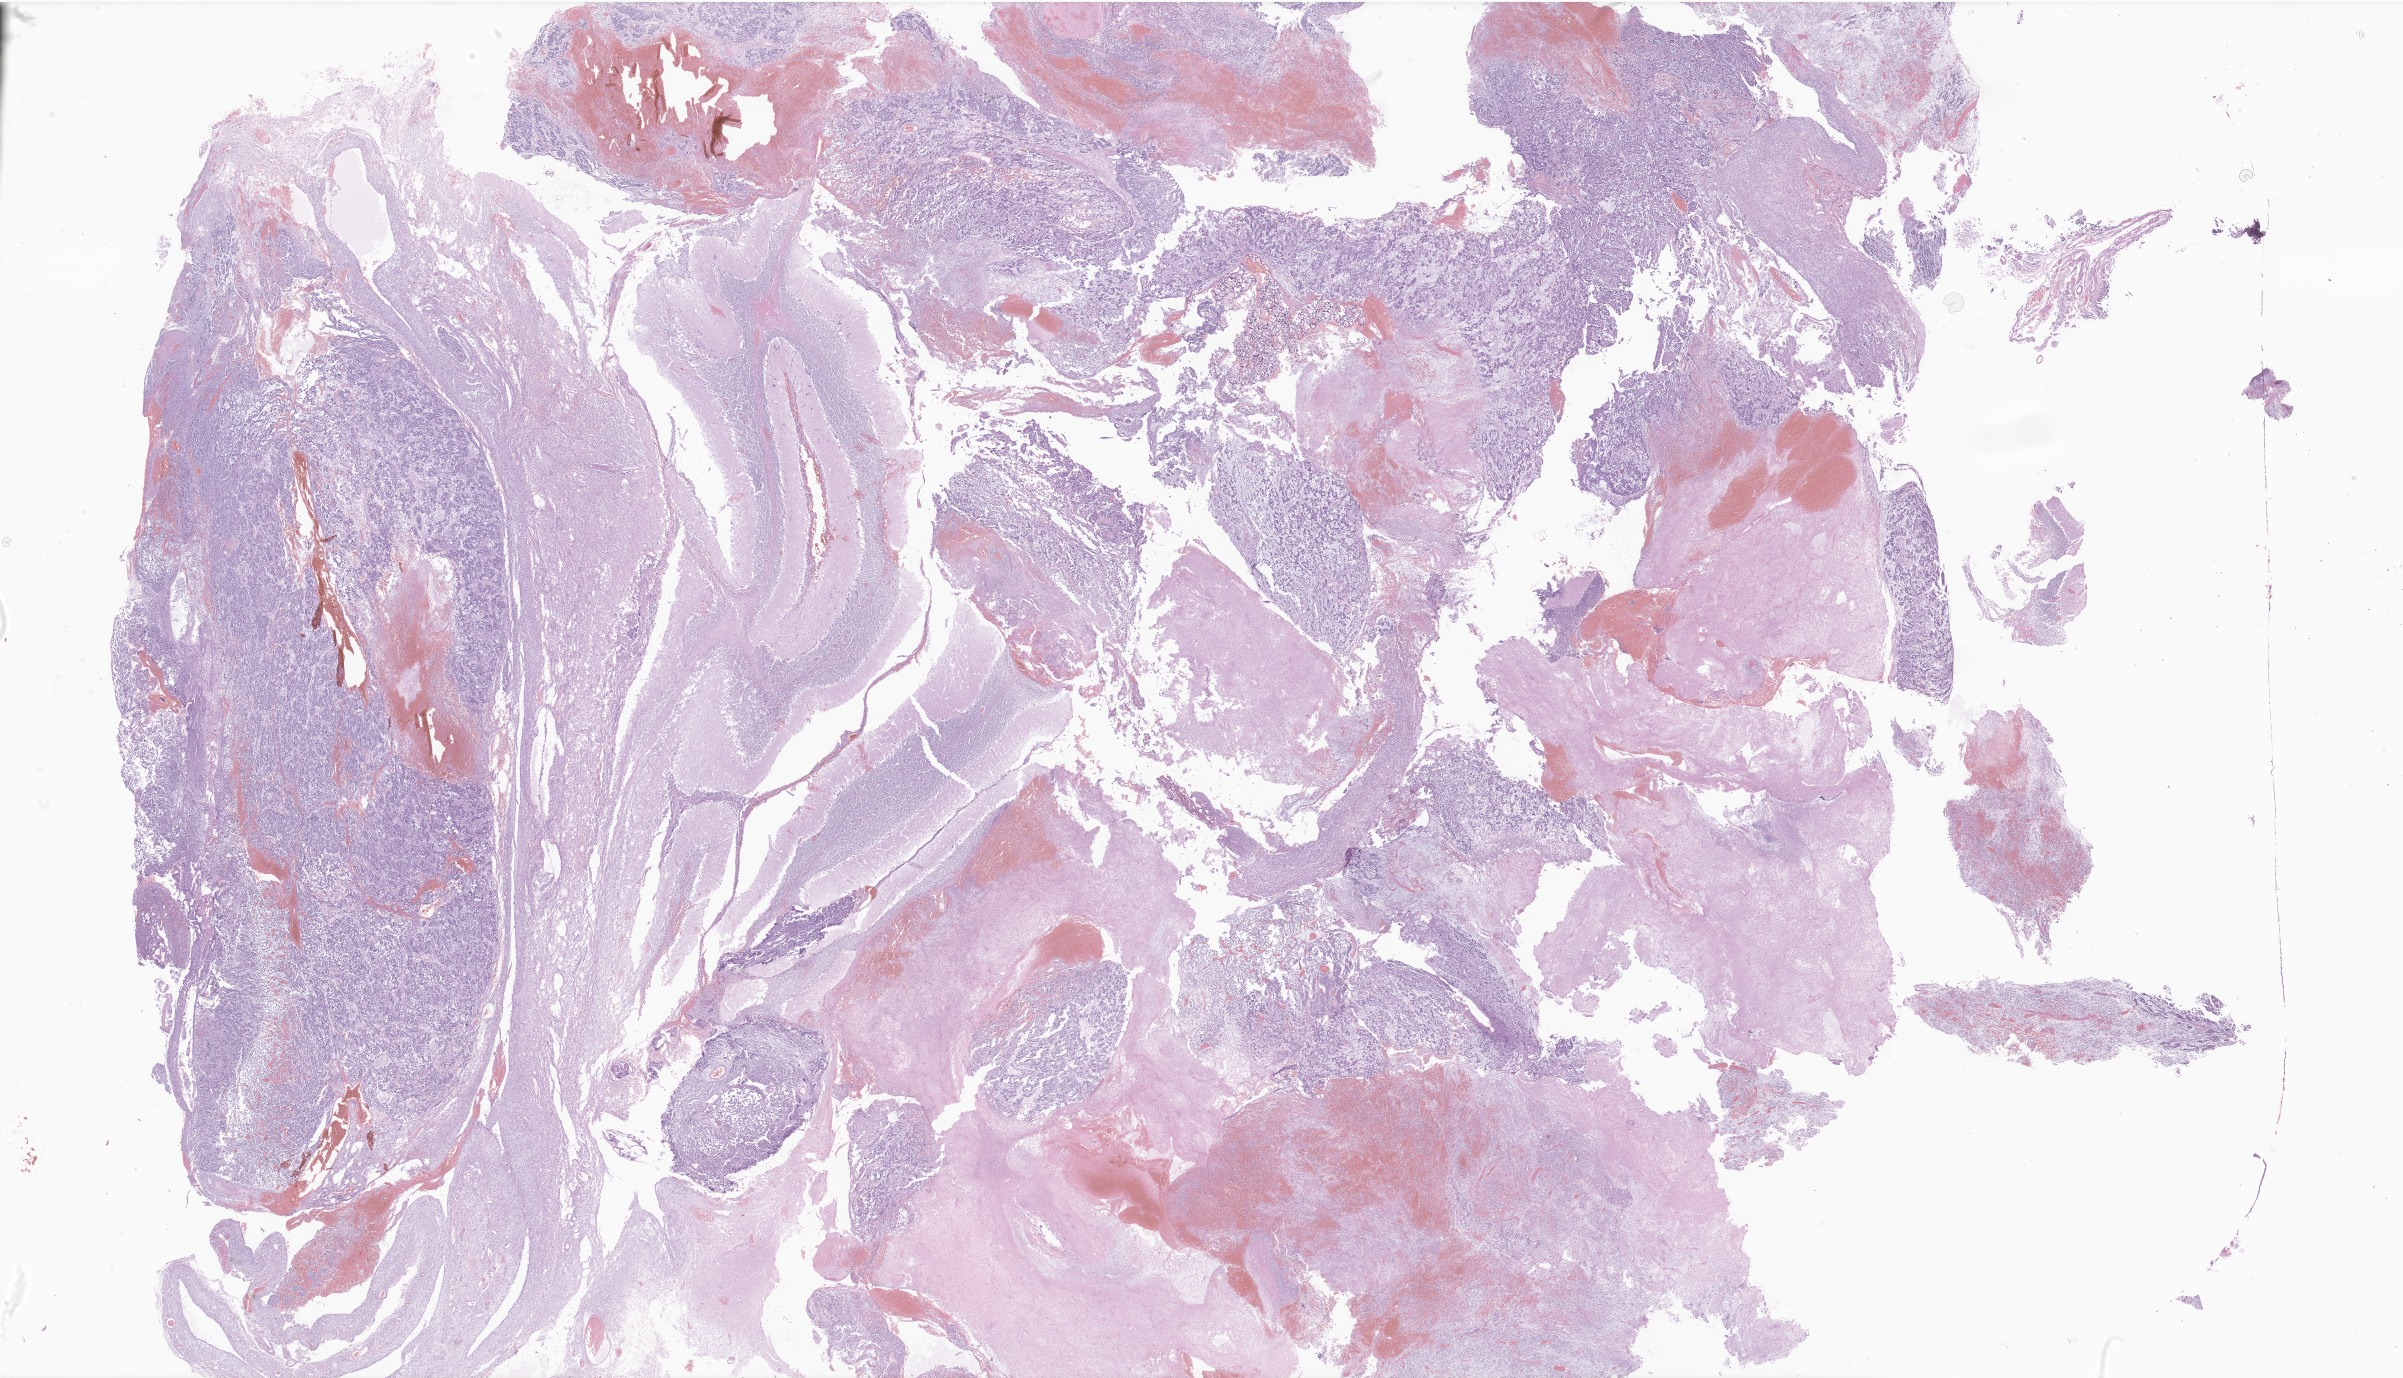
Haematoxylin and eosin whole-slide image of tumor tissue from the cerebellum — shown as a low-resolution overview of the whole scanned area (about 40.5 x 23.2 mm). Formalin-fixed, paraffin-embedded (FFPE) tissue. Patient male; age 106 months (8 years 10 months).
Diagnosis: Medulloblastoma, NOS.